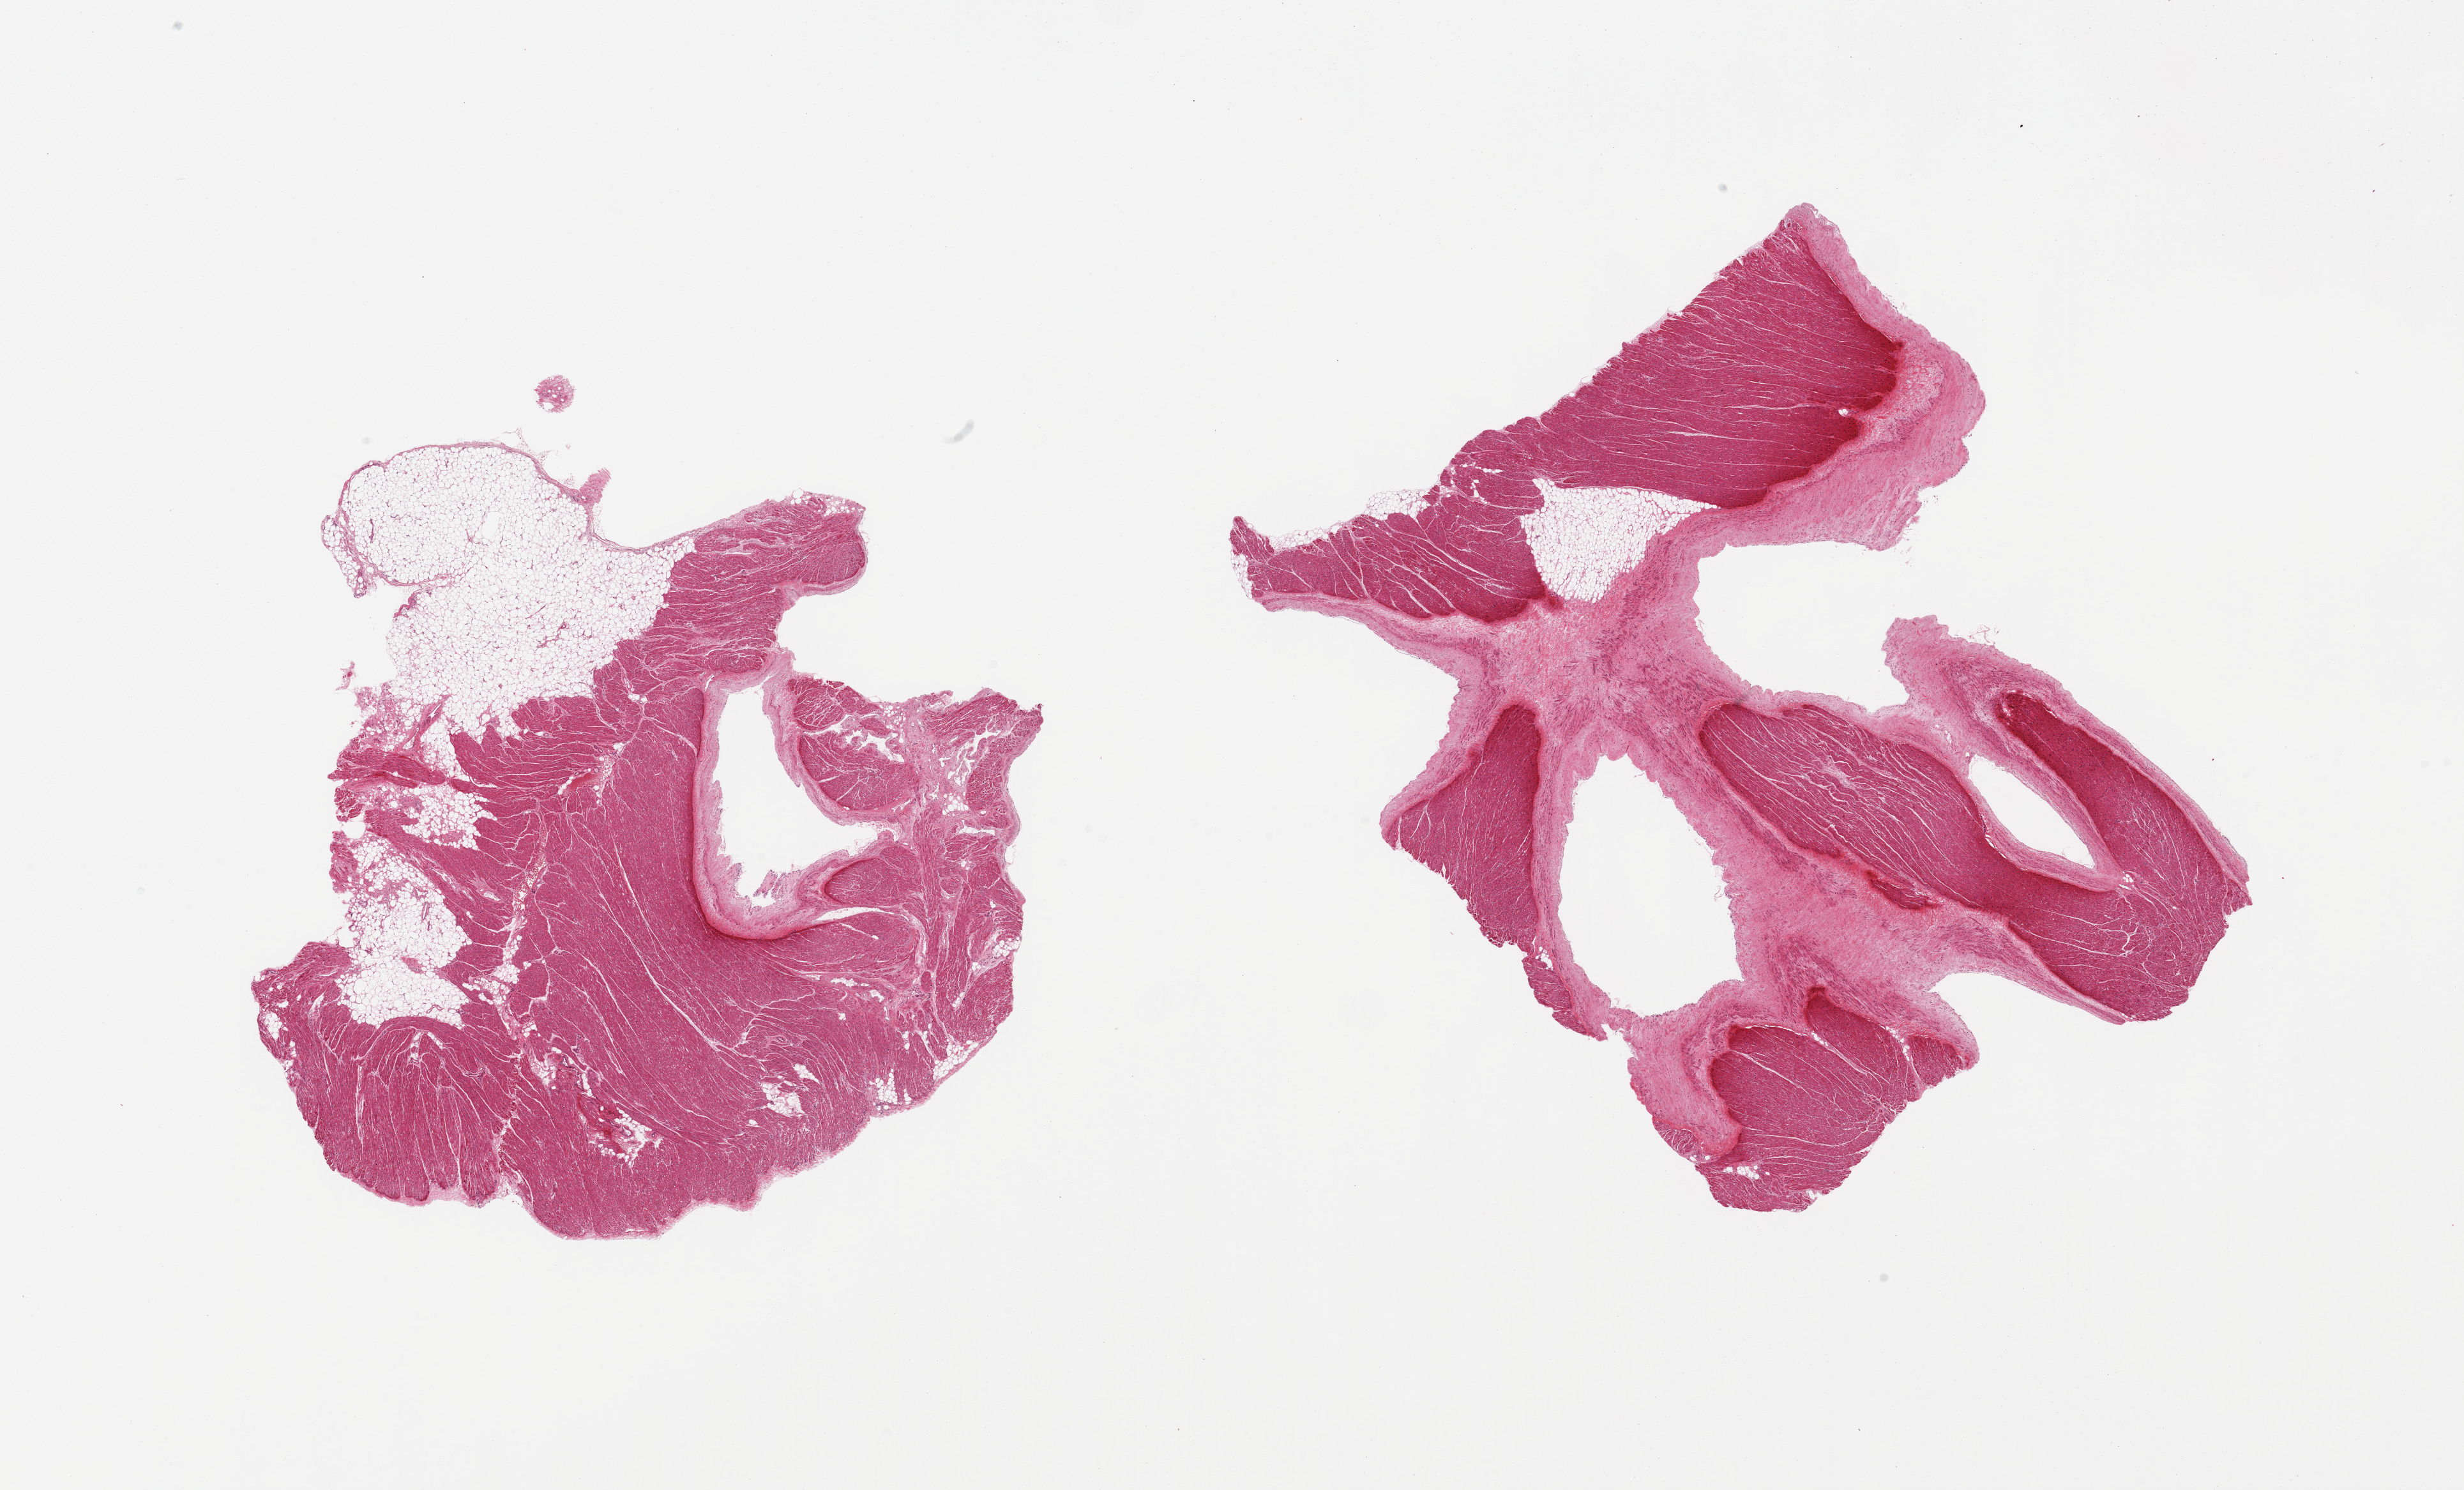
Whole-slide image, H&E stain, shown as a low-resolution overview of the whole scanned area (about 30.5 x 18.4 mm); PAXgene-fixed, paraffin-embedded tissue; sampled site (target tissue): auricular appendage; donor tissue sample. Donor sex: female.
Pathologist's review note for this sample: 2 pieces. 25% fat; prominent endocardial fibrous component up to 0.4 mm.